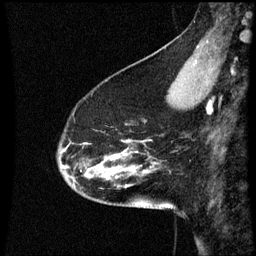
Breast MRI (dynamic contrast-enhanced), one sagittal slice. Slice 14 of 60 in the series (ordered by position). Dynamic contrast-enhanced series, image 2 of 3 at this slice position (ordered by acquisition). 1.5 T. TE 4.2 ms, TR 8.9 ms. 2 mm slice thickness. 256 × 256 image matrix, field of view 200 × 200 mm. Female patient, age 45 years. From the clinical record (not read from this slice): setting: breast cancer imaged before/during neoadjuvant chemotherapy; receptor status: HR-positive, HER2-negative.
Structures marked on this image (semi-automatically segmented with operator editing):
- analysis volume of interest (the breast-tissue region the enhancement analysis was run in; not a lesion): bounding box <58,94,171,205> (left, top, right, bottom; pixels)
- tumour enhancement mask (voxels above the 70 % enhancement threshold inside the analysis volume of interest): <114,154,127,159>